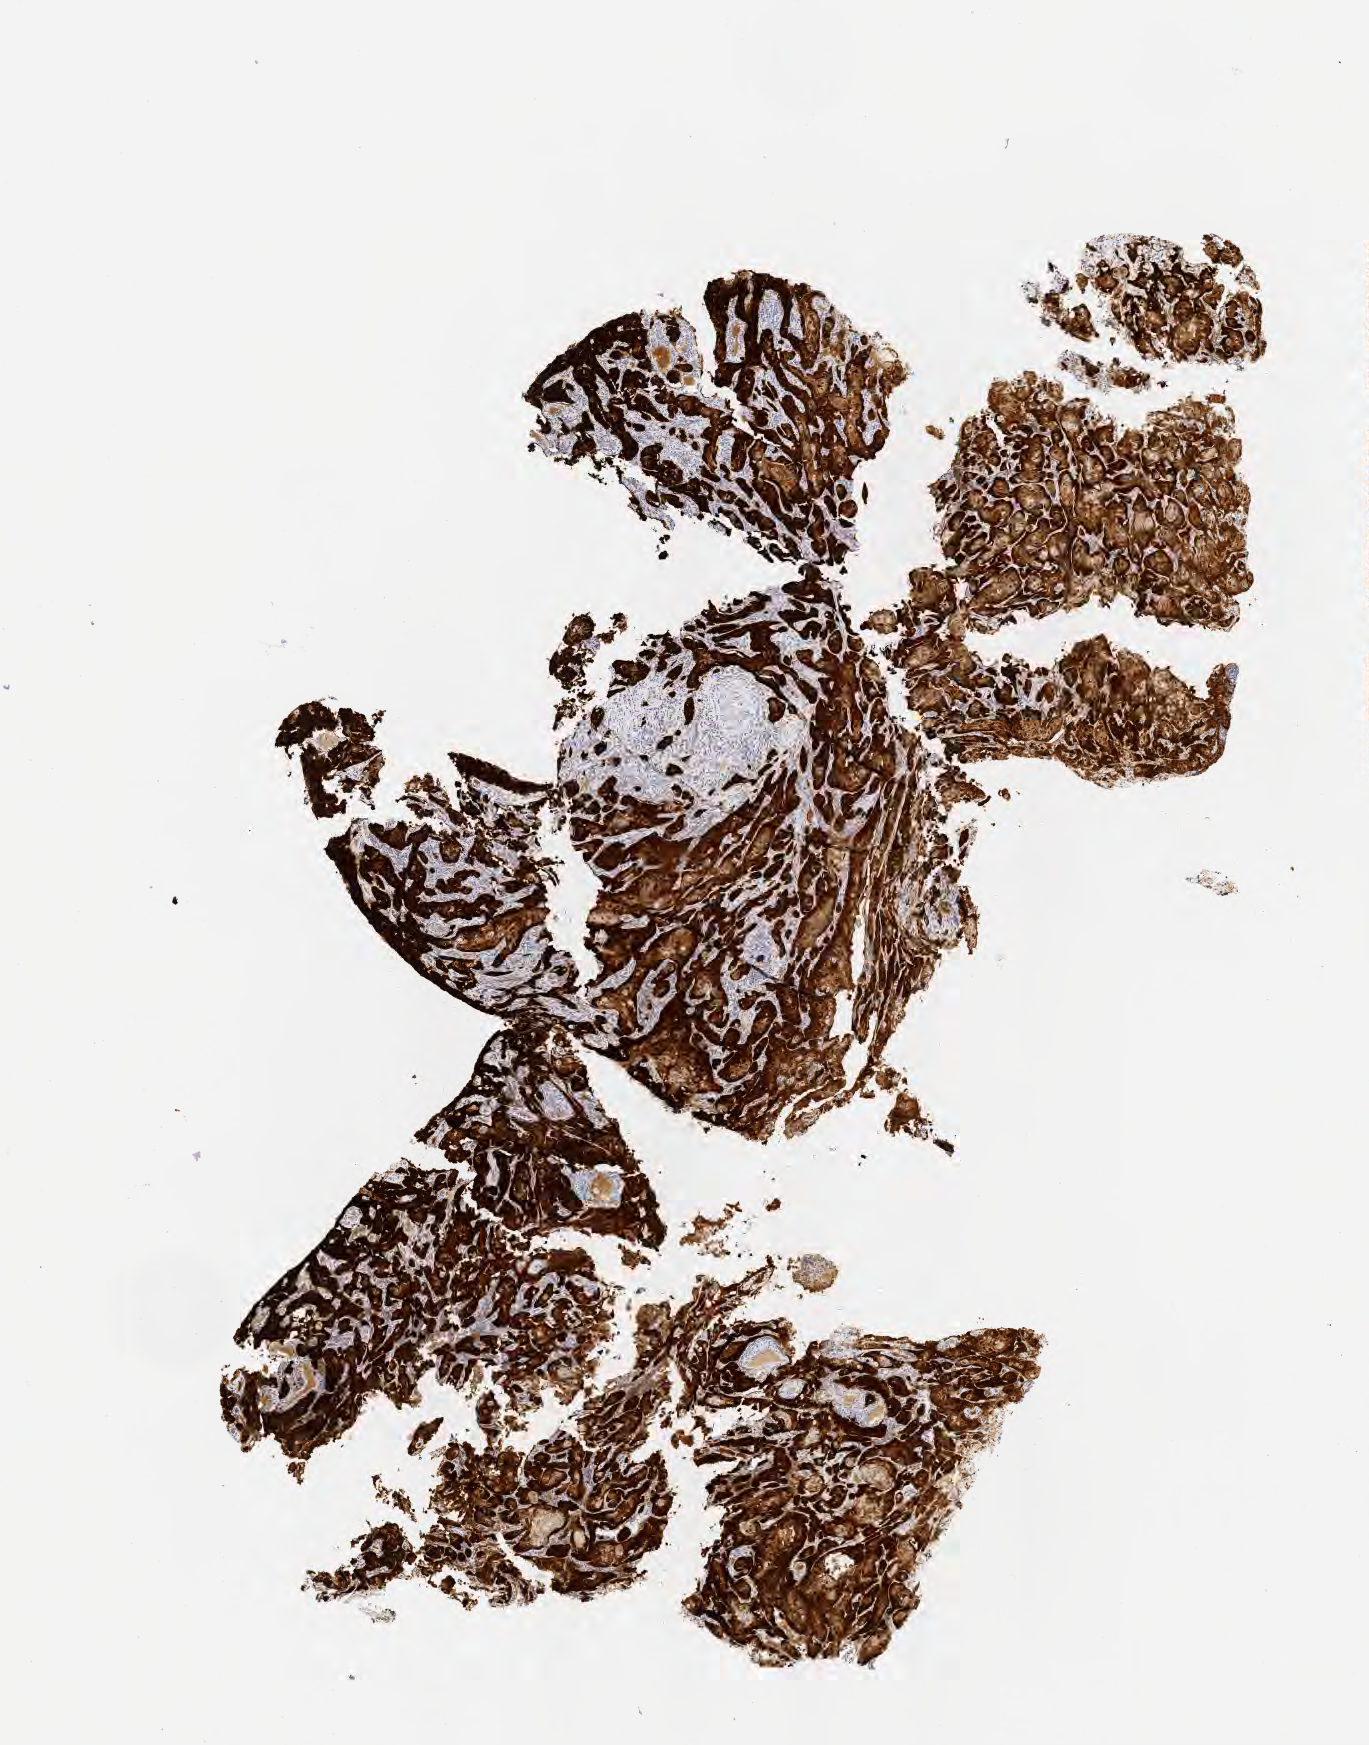
Whole-slide image, immunohistochemical stain for p16 (p16INK4a) — shown as a low-resolution overview of the whole scanned area (about 5.5 x 7.1 mm). Tumor tissue. Site: cervix. Patient female; 50 years old.
Histologic diagnosis: Squamous cell carcinoma, keratinizing, NOS.